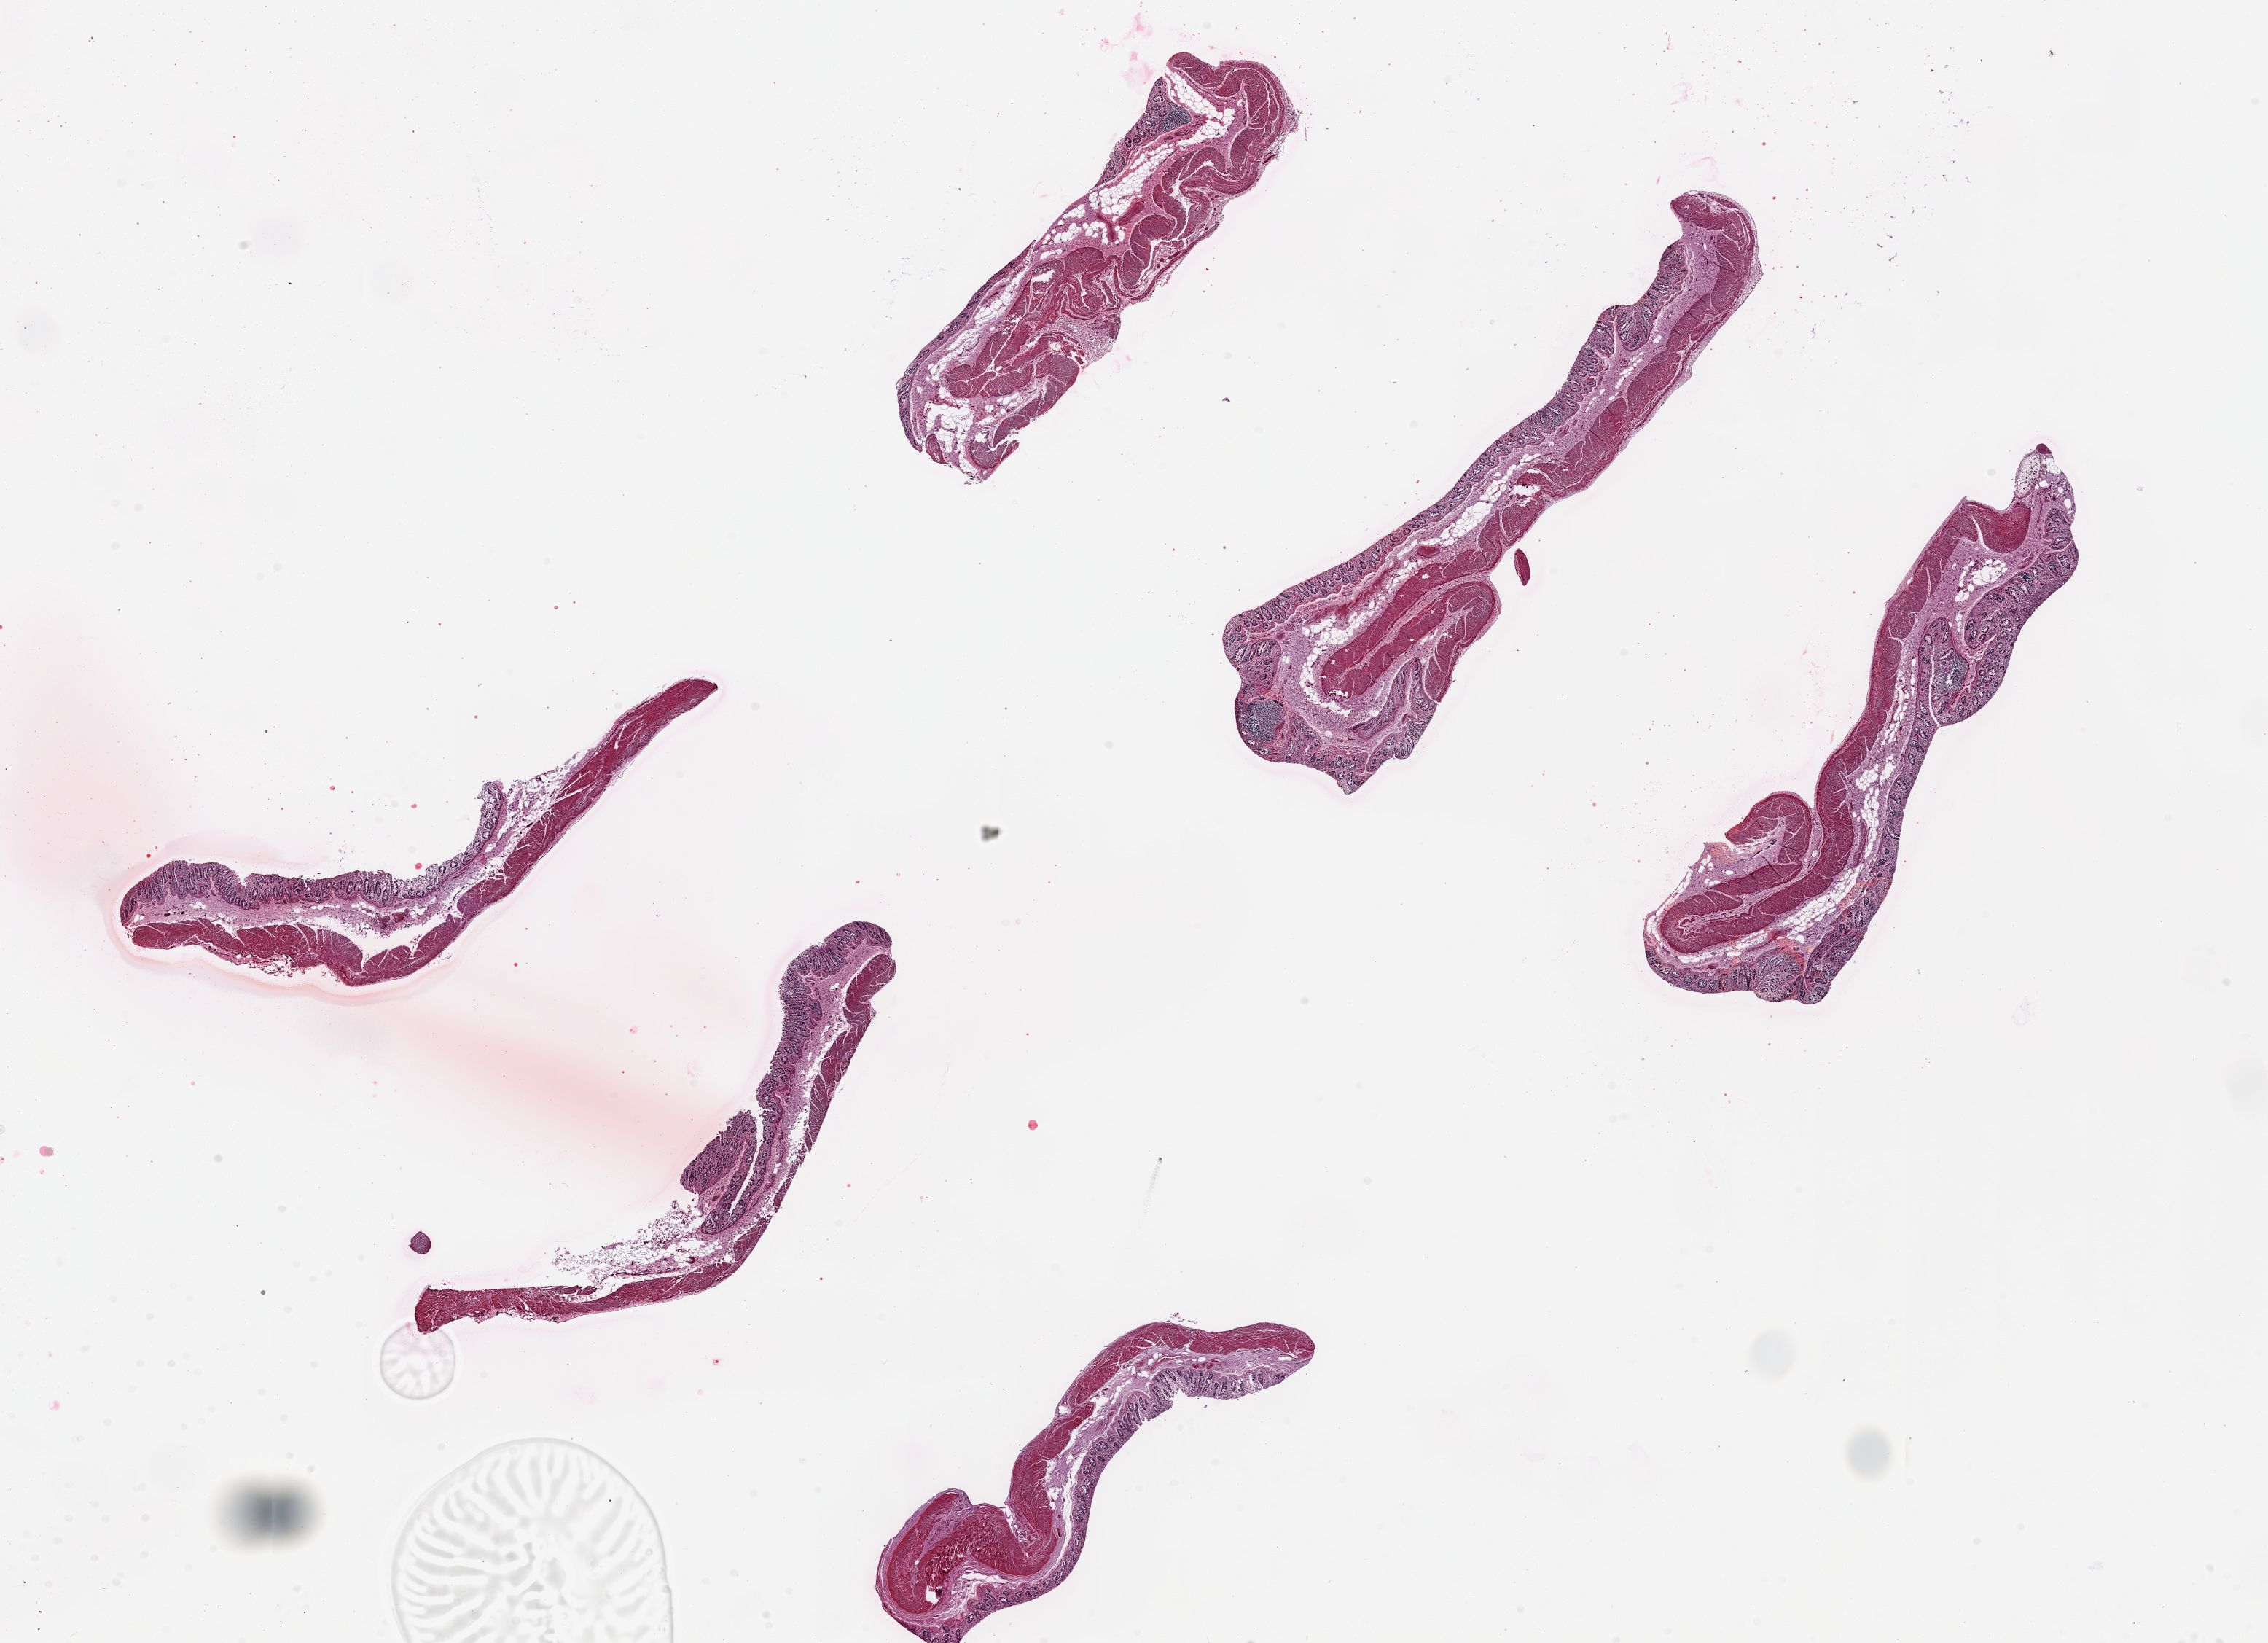
Digitized H&E-stained section, low-resolution overview of the scanned area, about 24.6 x 17.8 mm (slide scanned at 20x), PAXgene-fixed, paraffin-embedded tissue, target tissue: transverse colon, donor tissue sample. Donor: male.
Pathologist's review note for this sample: 6 pieces,~7x1.5mm; mucosa poorly preserved.